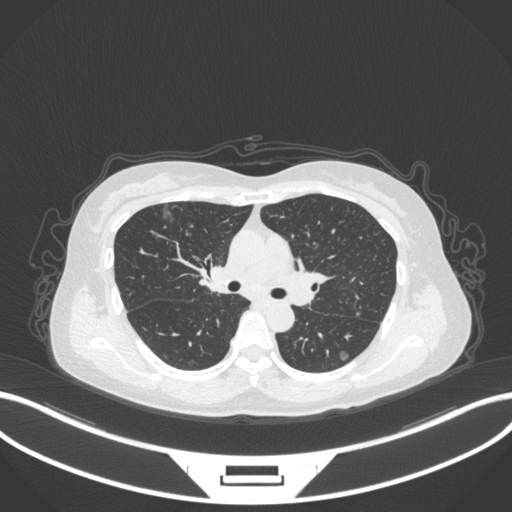
Chest CT, one axial slice; reconstruction kernel B31f; 120 kVp; lung window (W 1500 / L -600 HU); 1 mm slice thickness; 512 × 512 image matrix, field of view 400 × 400 mm. Patient: female, 61 years. Case-level facts recorded for this patient, not image findings: clinical TNM (as recorded): T1b N0 M0; histopathological grade: G1.
Outlined on this slice (rectangle marked by the reading radiologist):
- lung tumour (recorded histology: adenocarcinoma): box from (x=161, y=207) to (x=176, y=223) px